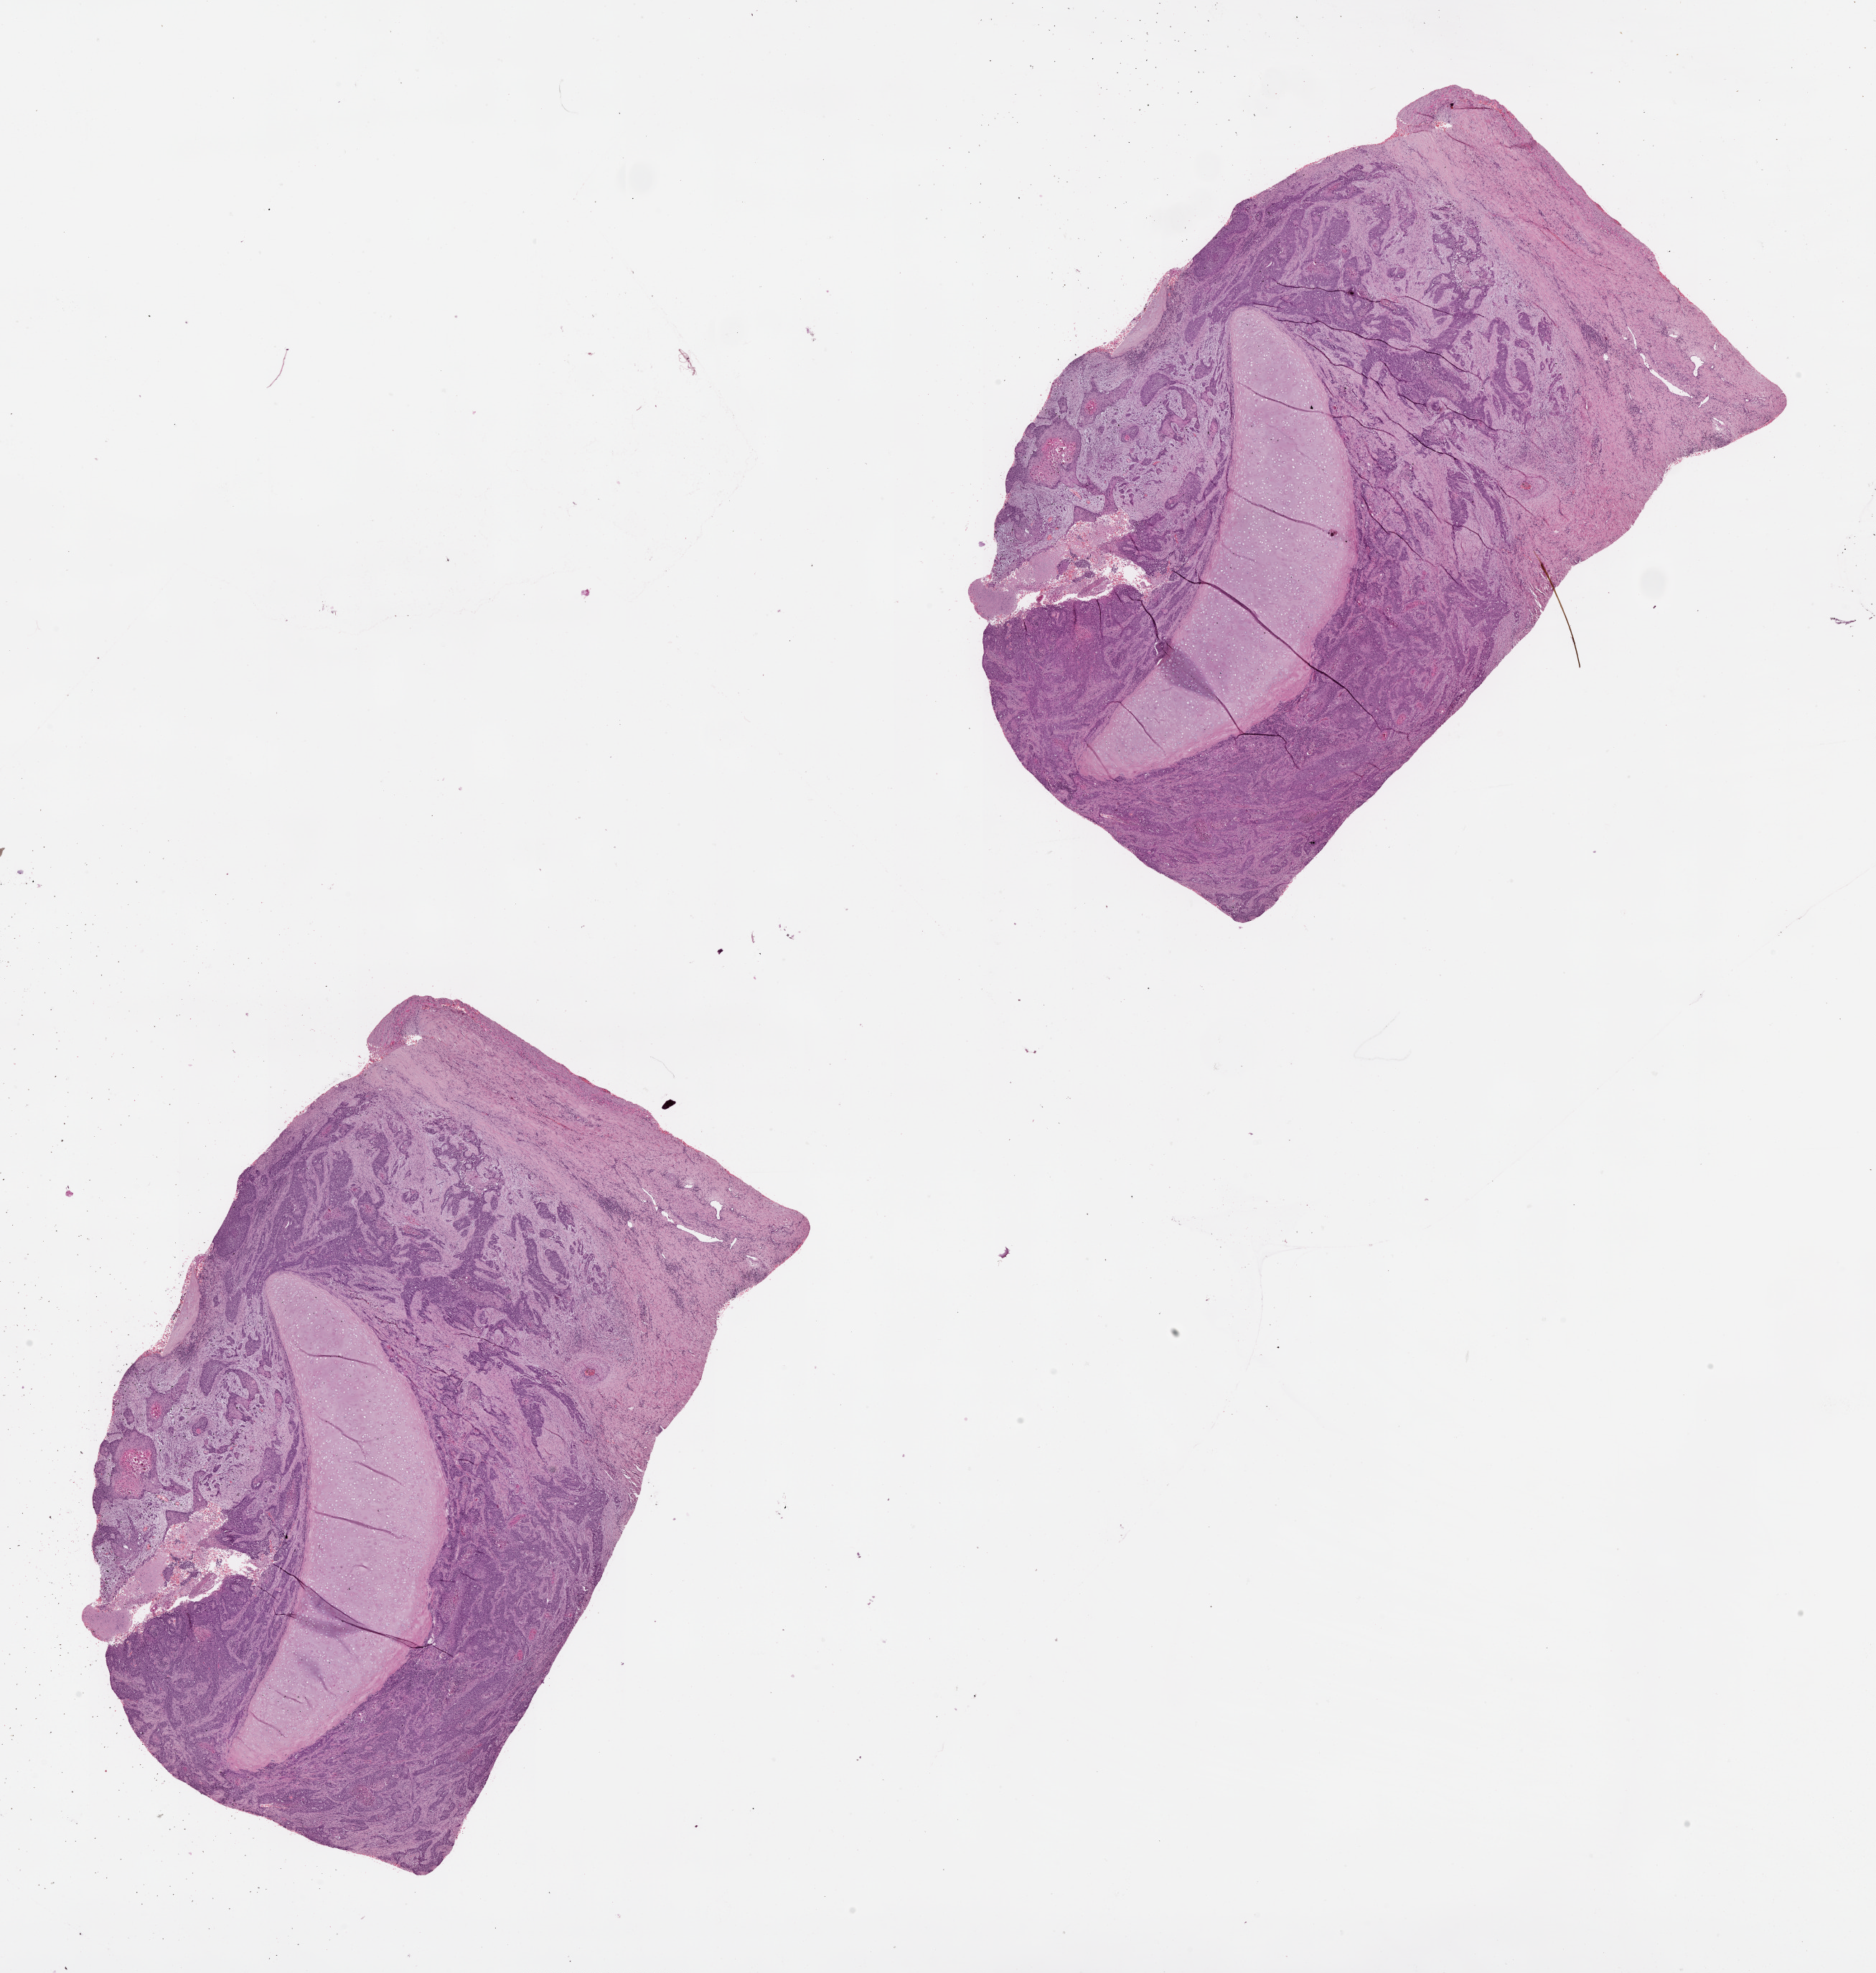
Hematoxylin and eosin (H&E) stained whole-slide image, a low-resolution overview of the entire scanned area, about 21.0 x 22.1 mm (acquisition: 20x scan); lung, tumour tissue. Patient: male, age 59 years.
Patient diagnosis (cohort enrolment): squamous cell carcinoma (lung).